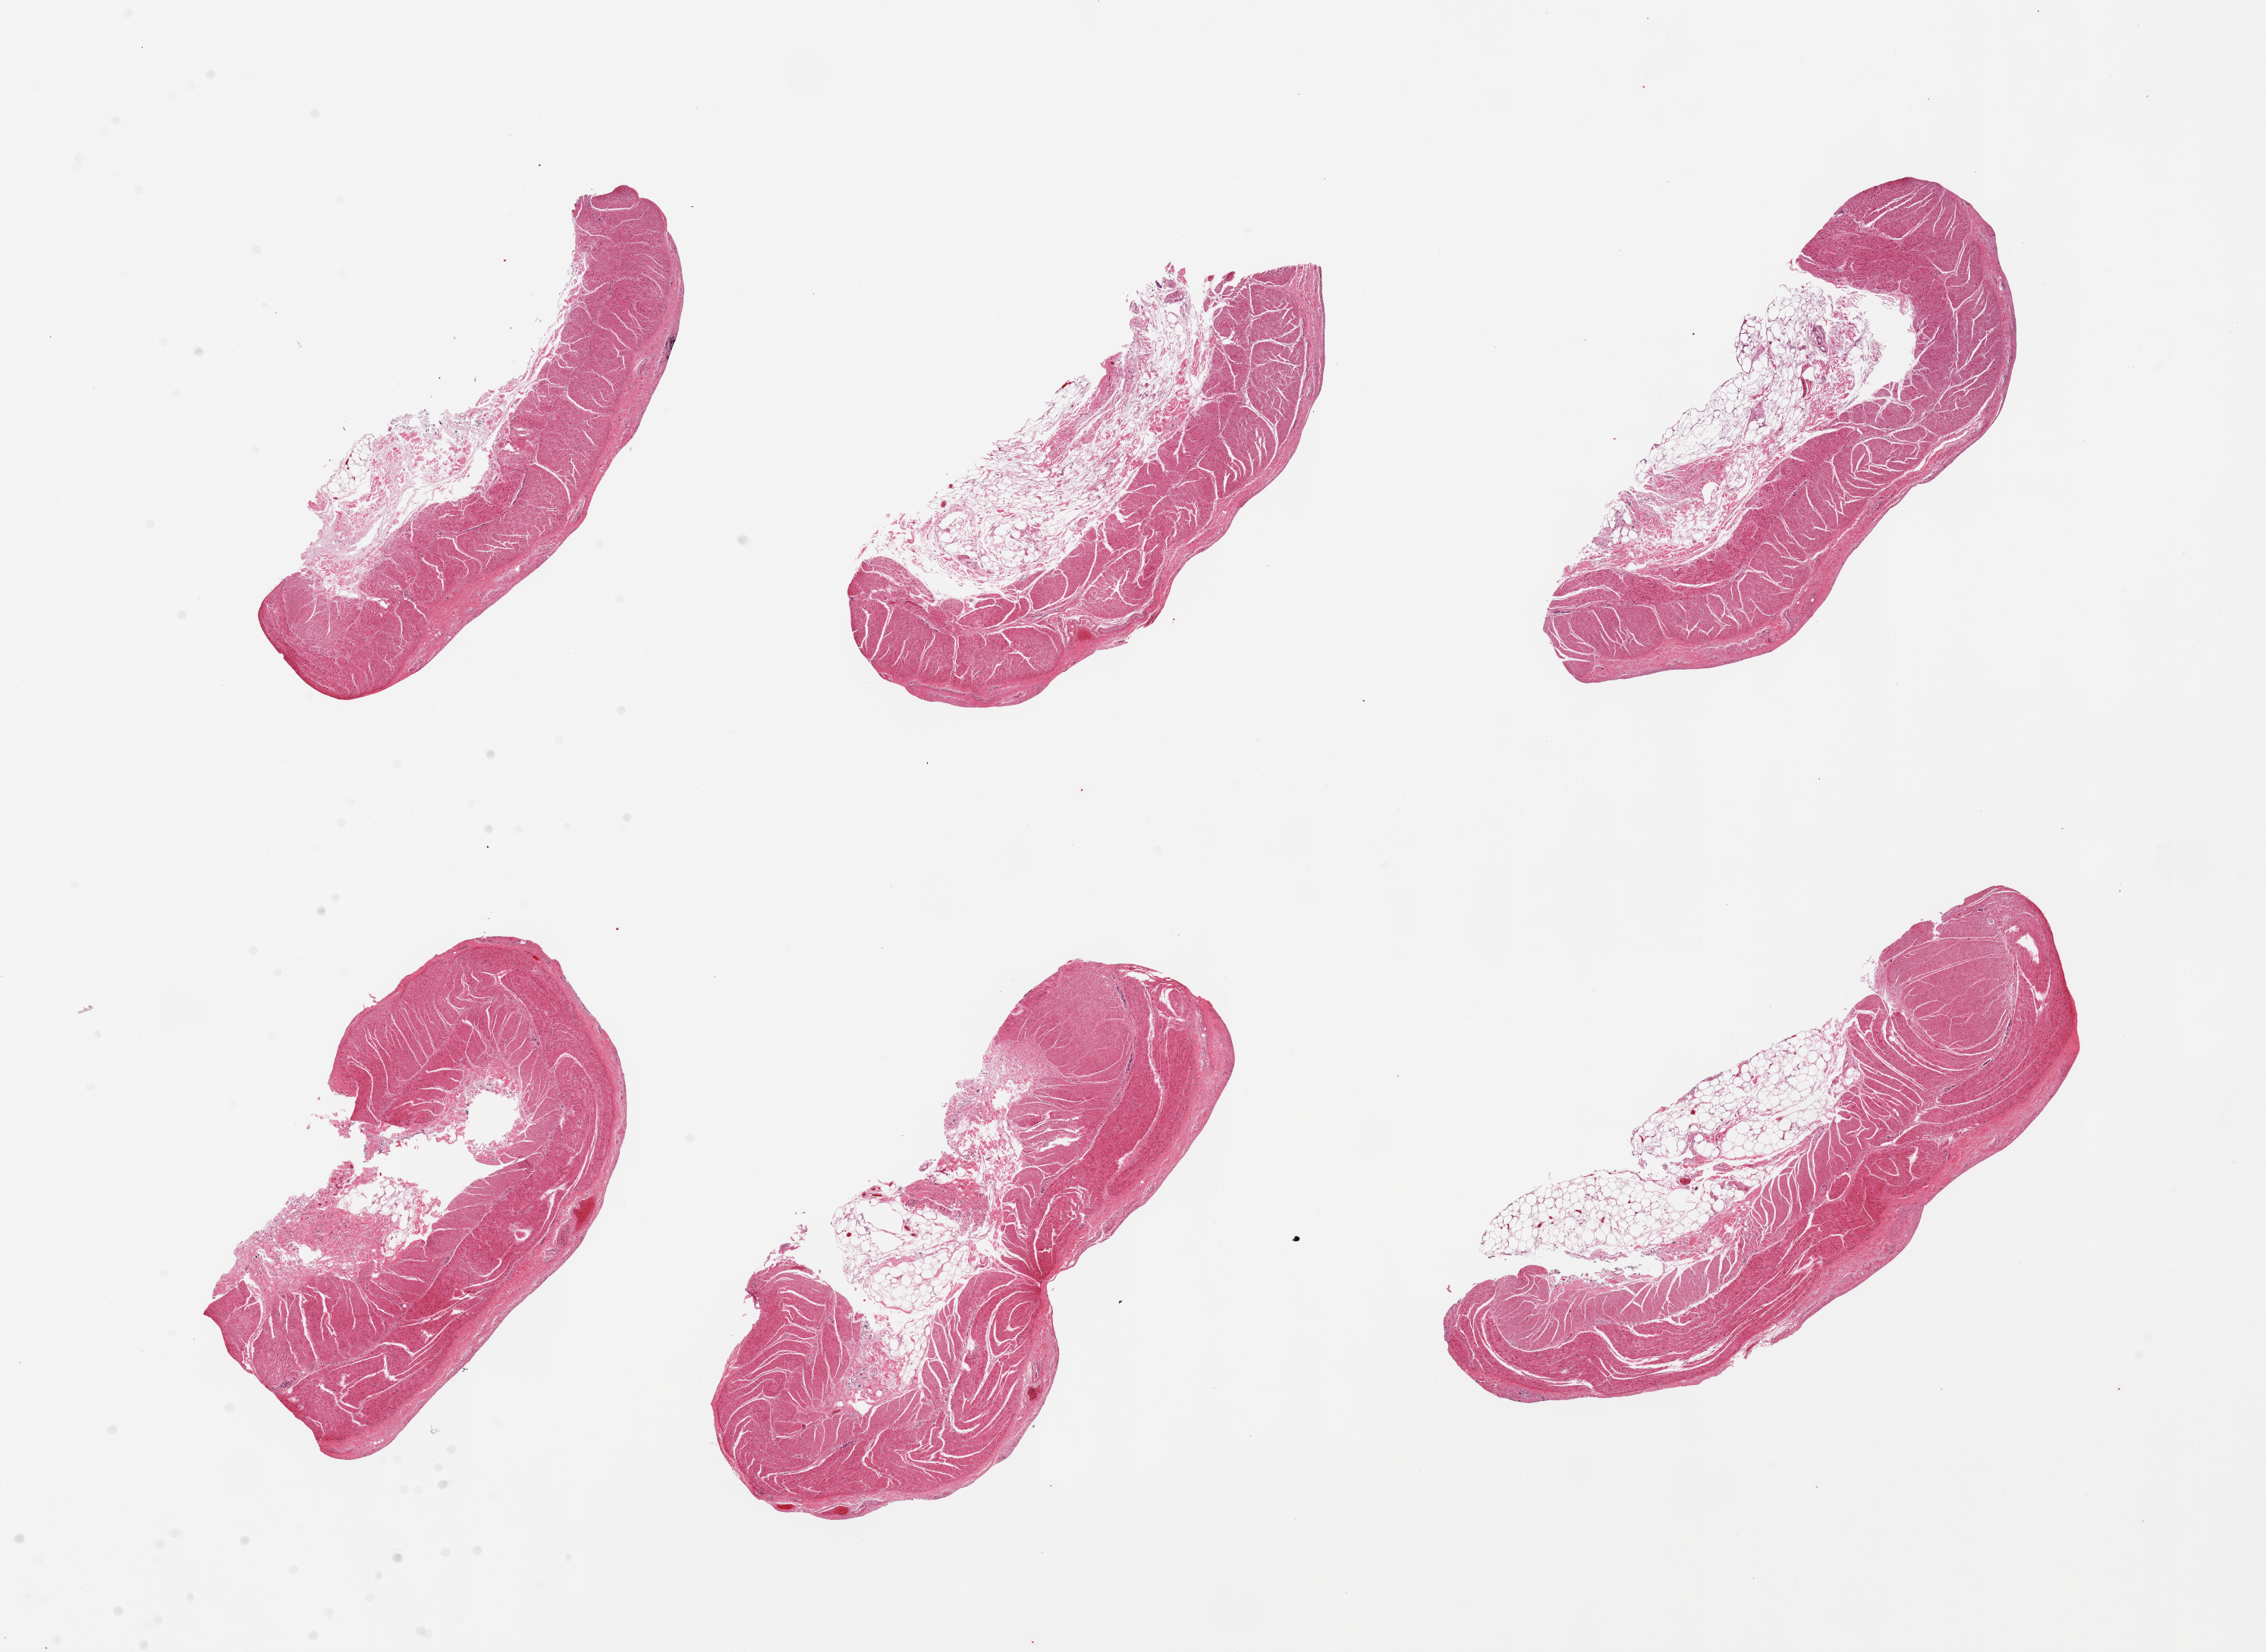
Digitized haematoxylin and eosin-stained section, brightfield, whole scanned area (about 23.6 x 17.2 mm, acquisition: 20x scan) shown as a low-resolution overview. PAXgene-fixed, paraffin-embedded tissue. Target tissue: sigmoid colon. Donor tissue sample. Donor: female.
Review note (as recorded): 6 pieces; target muscularis with attached fat up to 1.2mm.